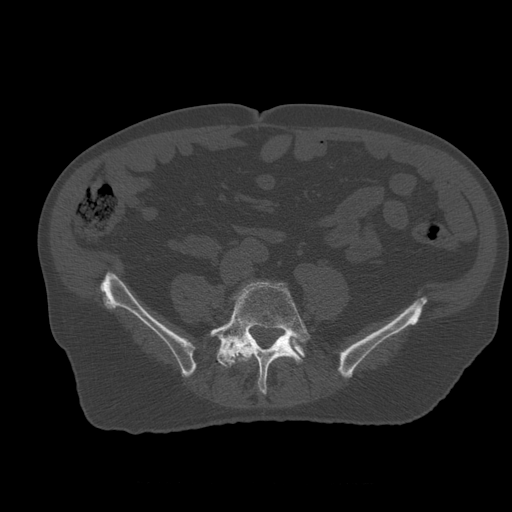
CT including the spine, one axial slice; reconstruction kernel STANDARD; 120 kVp; bone window (W 1800 / L 400 HU); 512 × 512 image matrix, field of view 407 × 407 mm. Patient age 73 years. From the clinical record (not read from this slice): primary cancer: prostate.
Outlined on this slice (semi-automatic segmentation, software-assisted and operator-edited):
- L4 vertebra: box from (x=236, y=345) to (x=258, y=362) px
- L5 vertebra: (x=210, y=282)–(x=311, y=394)